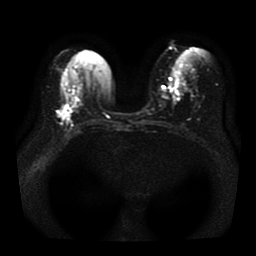
Breast MRI, one axial slice; position 18 of 41 along the scan axis; diffusion-weighted series; image 2 of 4 stored at this slice position (different b-values; order by instance number); 1.5 T; 5 mm slice thickness; 256 × 256 image matrix, field of view 330 × 330 mm. Female patient.
Outlined on this slice (outlined manually by an expert reader):
- tumour on diffusion-weighted imaging: bounding box (x1, y1, x2, y2) in pixels: (57, 105, 73, 120)